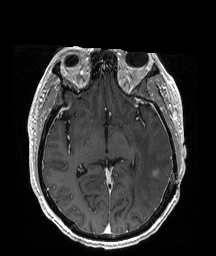
Brain MRI from a brain-tumour surgery series, one axial slice. Slice 103 of 192 in the series (ordered by position). T1-weighted post-contrast. 1 mm slice thickness. 216 × 256 image matrix, field of view 211 × 250 mm. From the clinical record (not read from this slice): histopathology: Glioblastoma; WHO grade: 4; IDH mutation: no.
Structures marked on this image (manually delineated by an expert):
- tumour: bounding box (x1, y1, x2, y2) in pixels: (146, 167, 150, 173)